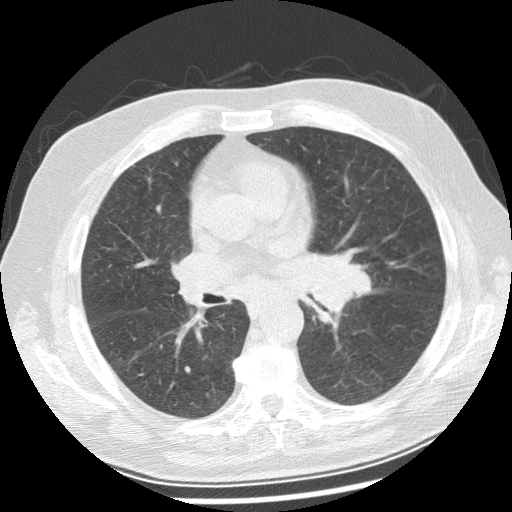
Low-dose screening chest CT, one axial slice; position 137 of 250 along the scan axis; lung window (W 1500 / L -600 HU); 2.5 mm slice thickness; 512 × 512 image matrix.
Outlined on this slice (expert manual segmentation):
- lesion 1 (tumor, left main bronchus): box from (x=311, y=265) to (x=371, y=313) px